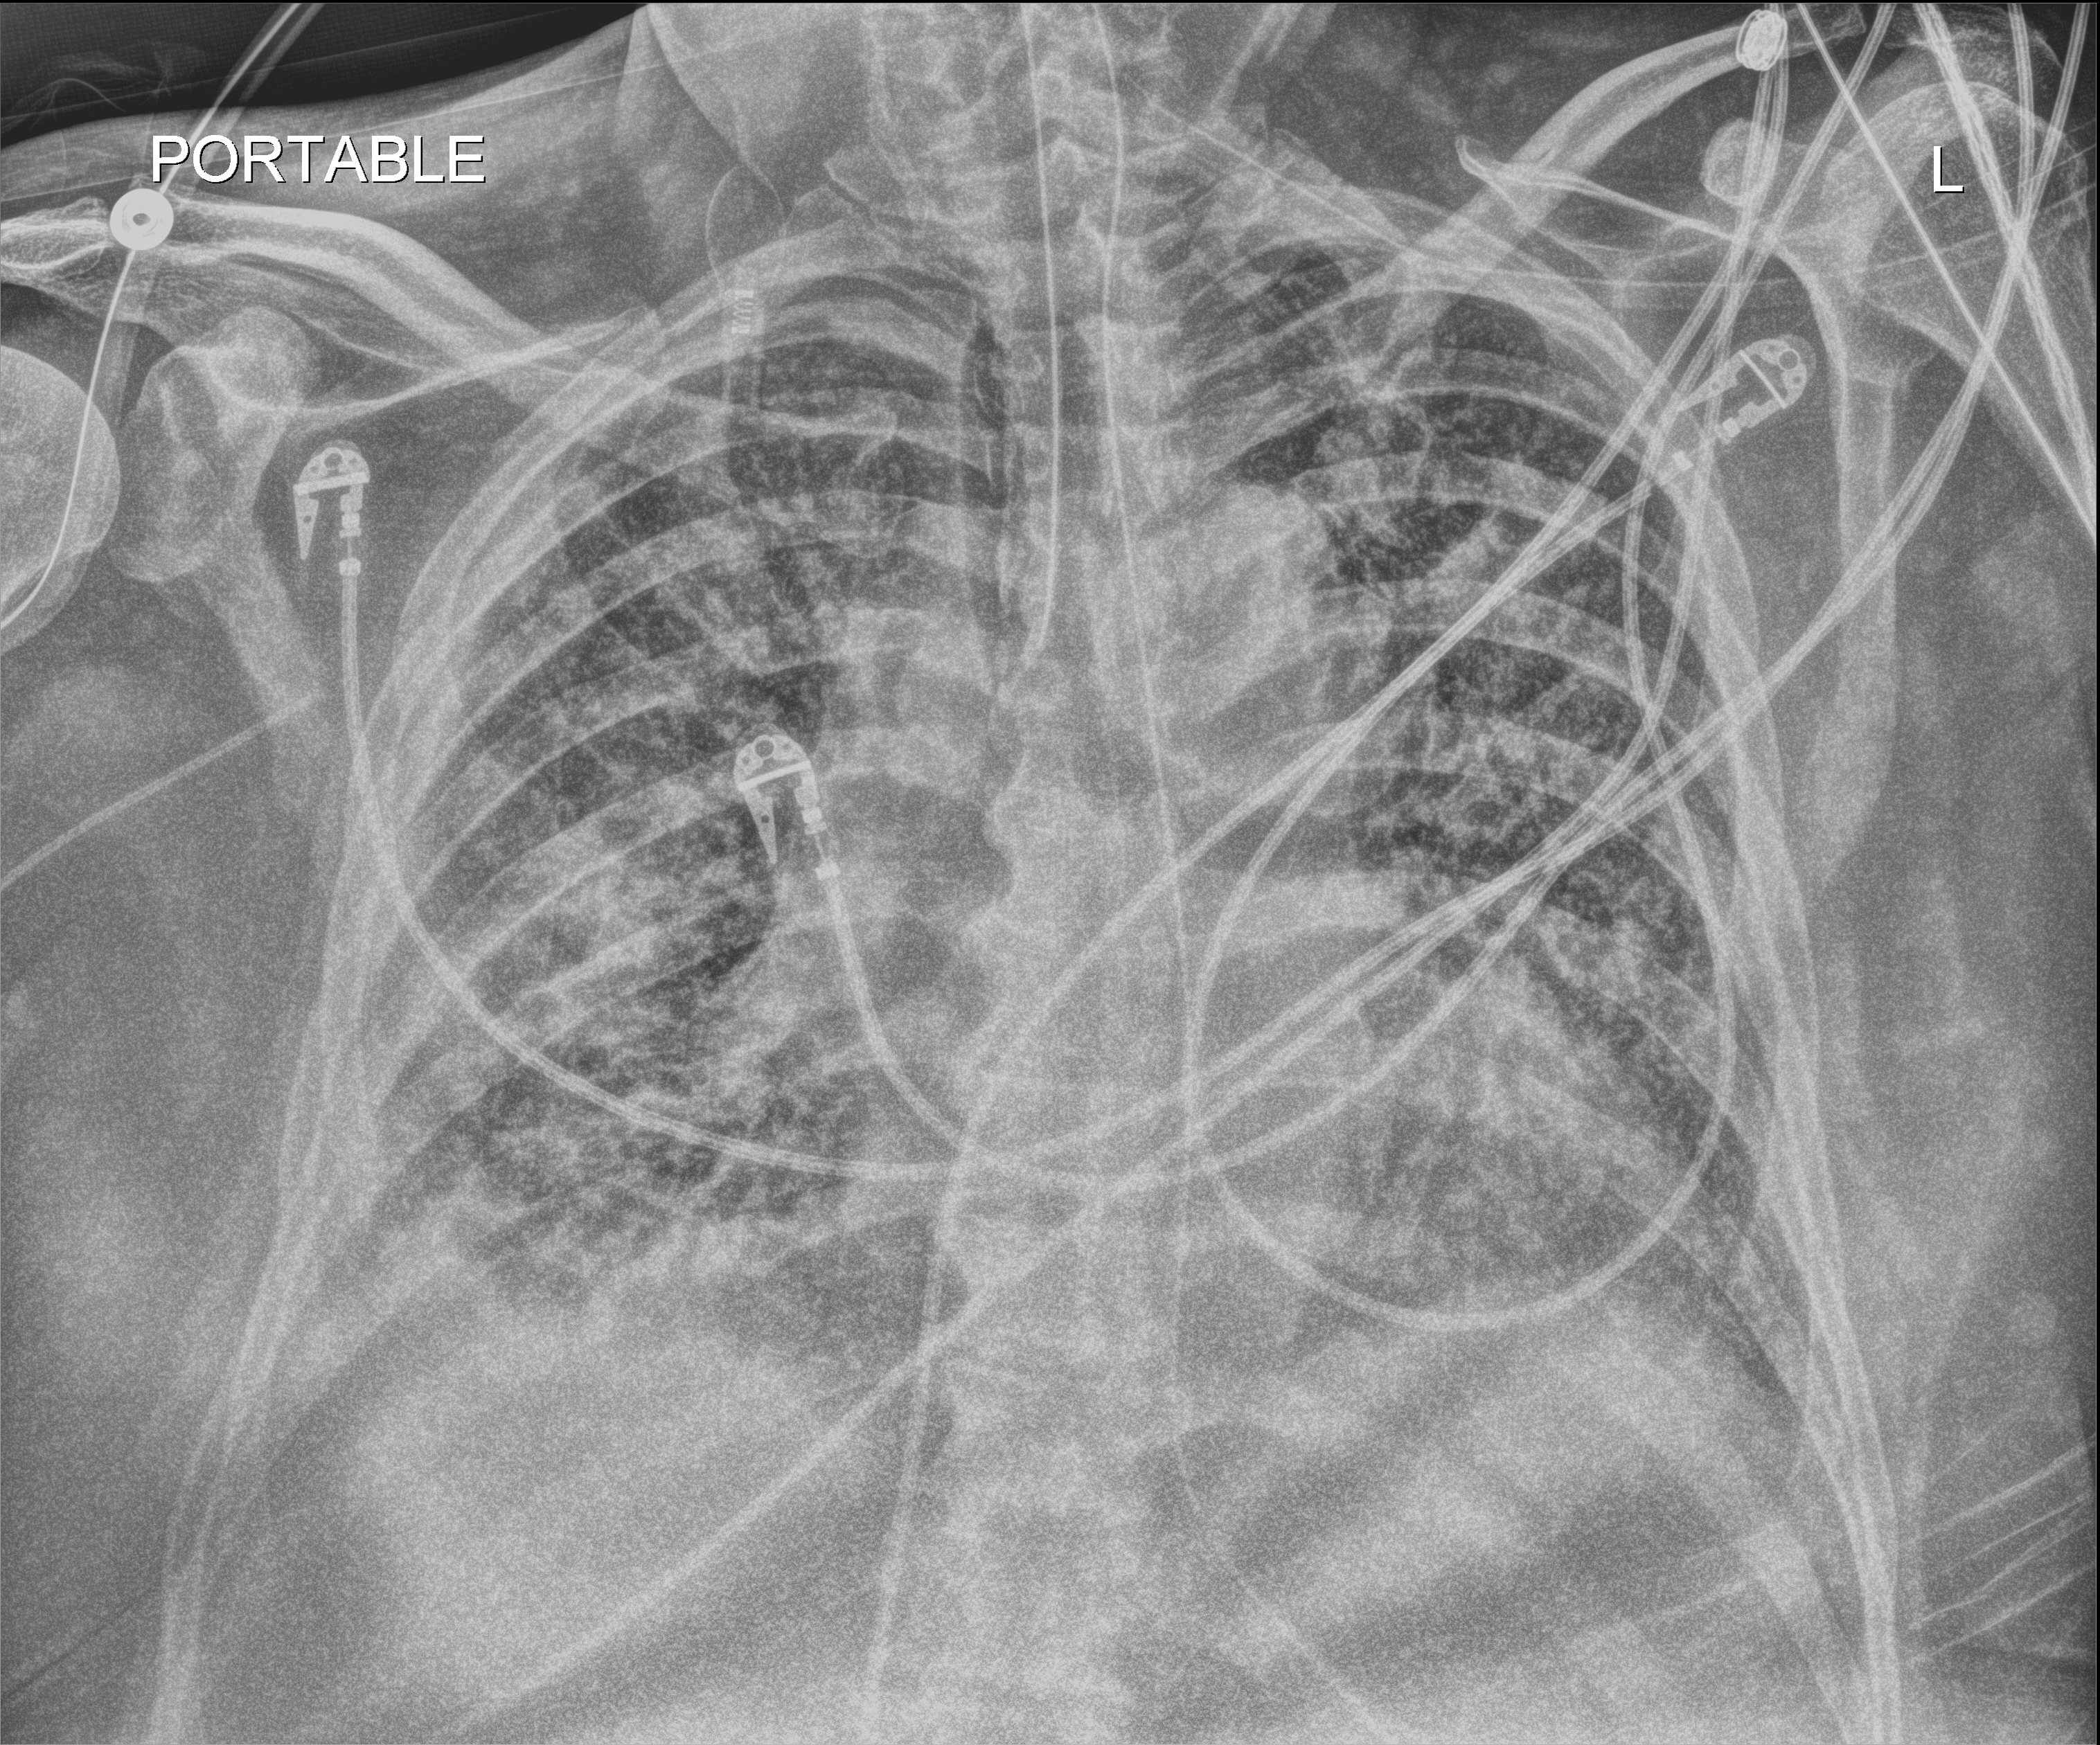
Chest X-ray (portable), anteroposterior (AP) projection. Male patient hospitalised with COVID-19, age 60–74 years.
Hospital-stay facts (about this admission, not read from this image; timing relative to this image not recorded):
- mechanically ventilated during this hospital stay: yes
- admitted to intensive care during this hospital stay: yes
- length of hospital stay: 40 days